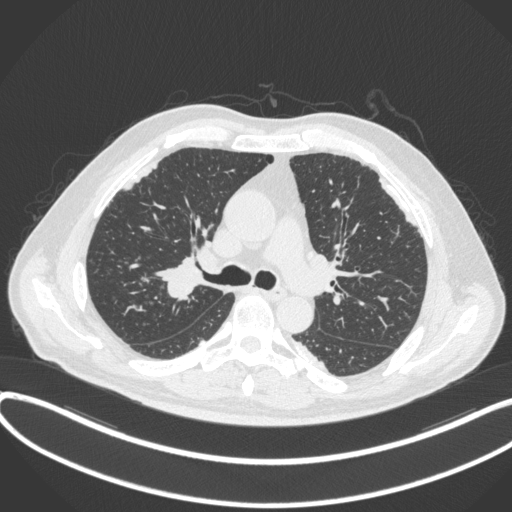
Chest CT, one axial slice. Slice 270 of 455 in the series (ordered by position). Lung window (W 1500 / L -600 HU). 1 mm slice thickness. 512 × 512 image matrix, field of view 400 × 400 mm. Male patient, age 58 years. Case-level facts recorded for this patient, not image findings: clinical TNM (as recorded): T1c N0 M0.
Annotated regions visible in this slice (bounding box drawn by a radiologist):
- lung tumour (recorded histology: squamous cell carcinoma): bounding box <153,256,208,300> (left, top, right, bottom; pixels)